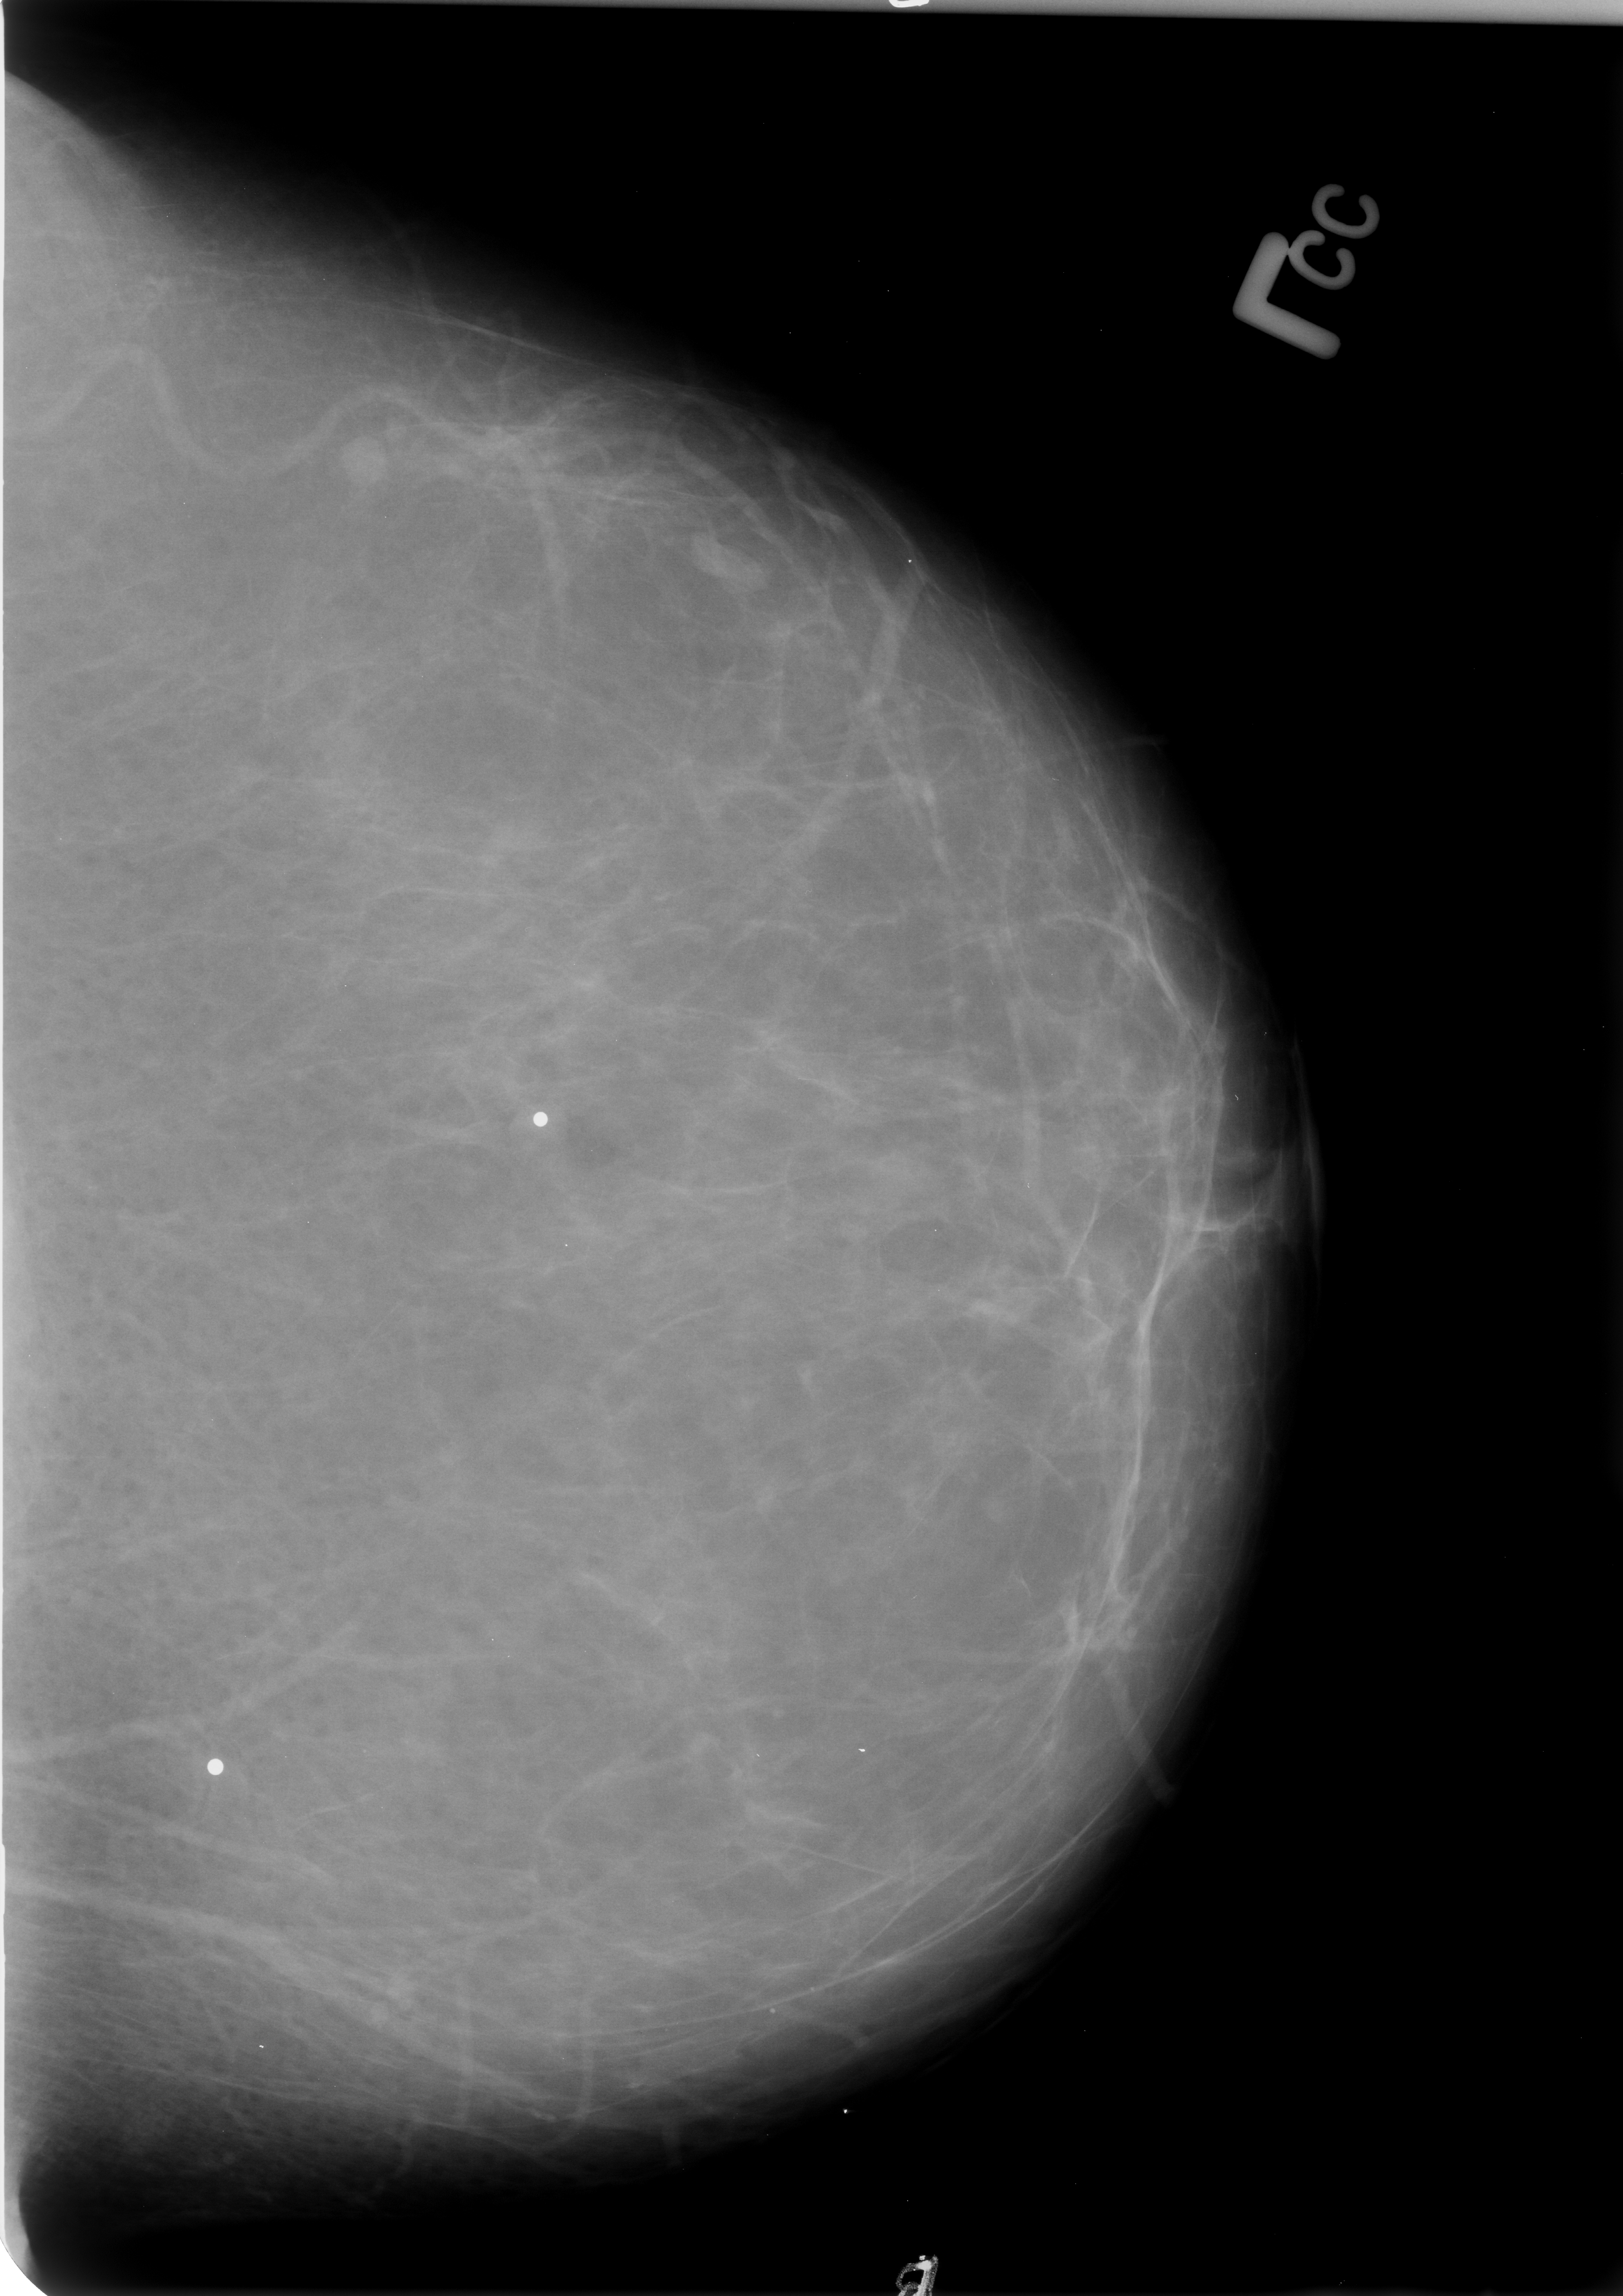
Mammogram (digitized film); left breast; CC view; 1623 × 2296 image matrix.
Marked abnormalities (boxes around the expert regions of interest):
- Finding 1 of 2: mass, shape lymph node, margins circumscribed; BI-RADS assessment category 3; subtlety rating 2 on a 1 (subtle) to 5 (obvious) scale; outcome (as recorded, no biopsy): benign without callback (not worked up further): bounding box (x1, y1, x2, y2) in pixels: (323, 426, 403, 512)
- Finding 2 of 2: mass, shape lymph node, margins circumscribed; BI-RADS assessment category 3; benign; no additional work-up was recommended (outcome (as recorded, no biopsy): benign without callback): (684, 515, 774, 596)